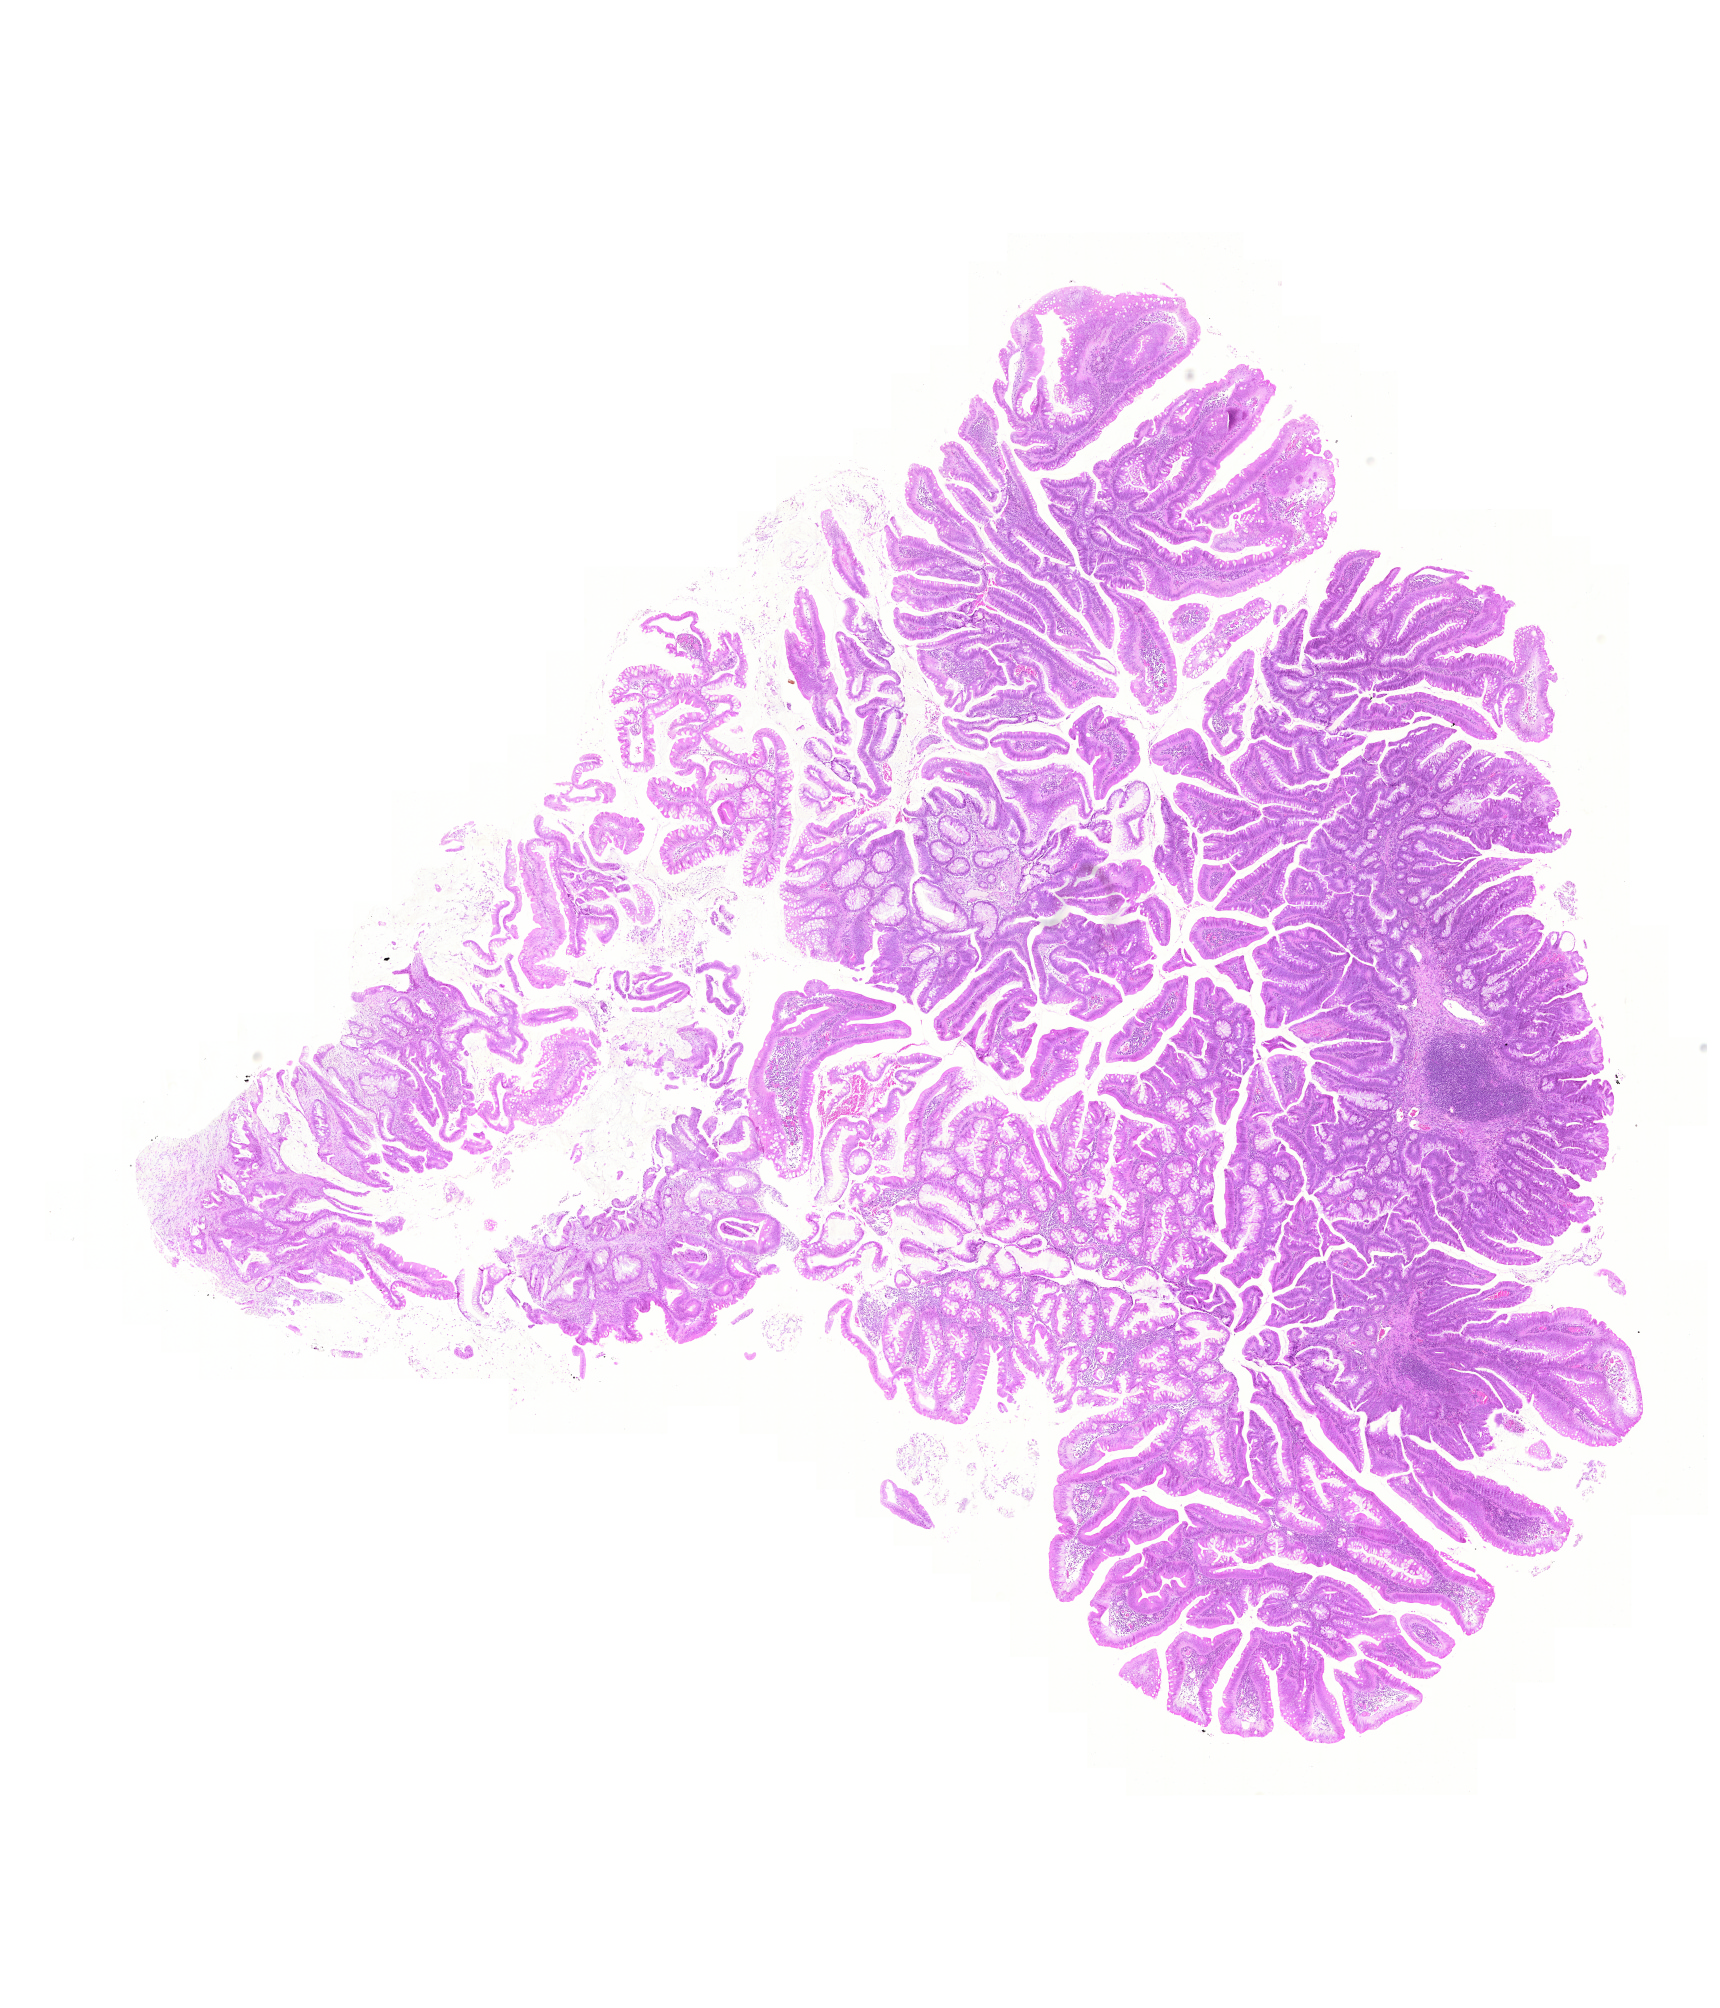
Digitized Hematoxylin and eosin (H&E) stained tissue section (whole slide) — shown as a low-resolution overview of the whole scanned area (about 12.8 x 14.9 mm, from a 20x scan). Formalin-fixed paraffin-embedded (FFPE) diagnostic section. Sample: primary tumour, colon. Patient sex: female.
Diagnosis: Mucinous adenocarcinoma (cecum).